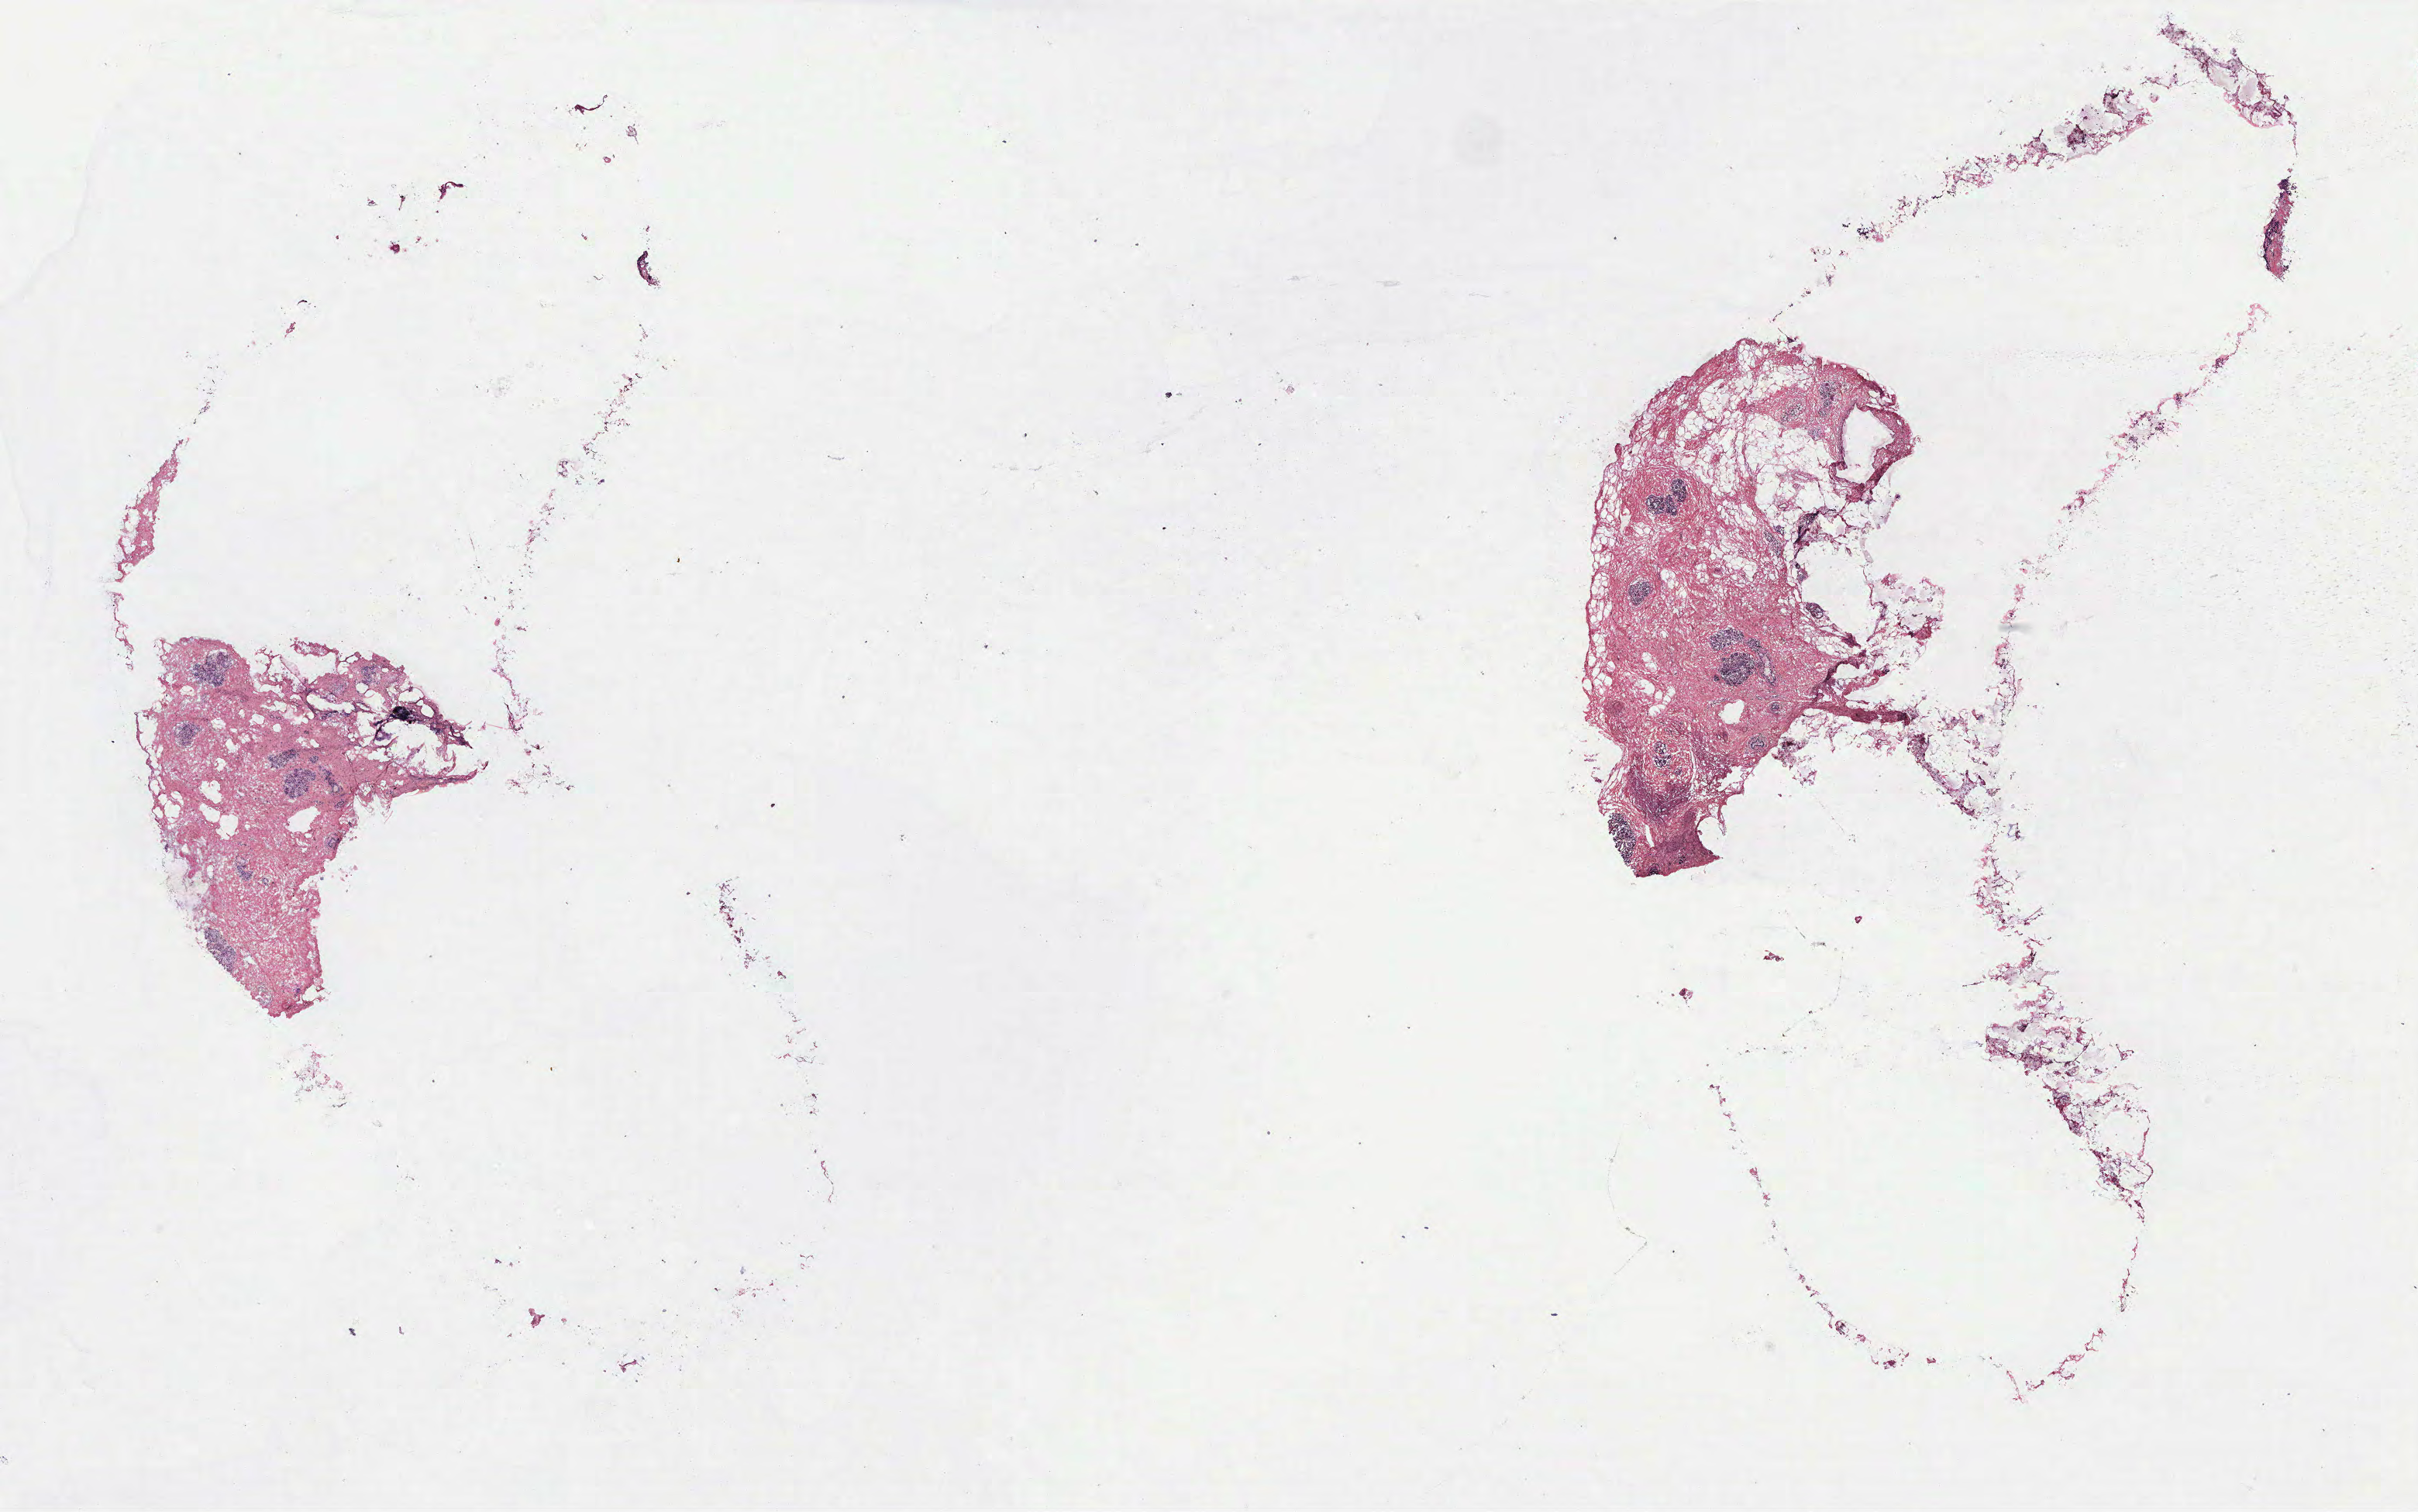
Whole-slide histology image, H&E-stained — low-resolution overview of the scanned area, about 25.0 x 15.6 mm (from a 40x scan). Breast, tissue type not recorded.
* patient diagnosis (cohort enrolment): breast cancer (breast)